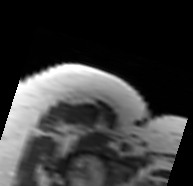
MRI of an extremity soft-tissue mass, one axial slice. MR volume resampled by the dataset authors to the PET/CT grid (not the native acquisition matrix). 193 × 186 image matrix. Female patient. From the clinical record (not read from this slice): histological type: malignant solitary fibrous tumor; grade: intermediate; site of the primary tumour: right thigh.
Structures marked on this image (expert contour drawn on MRI and transferred to this co-registered scan by the dataset authors):
- gross tumour volume including surrounding oedema: bounding box (x1, y1, x2, y2) in pixels: (54, 121, 109, 150)